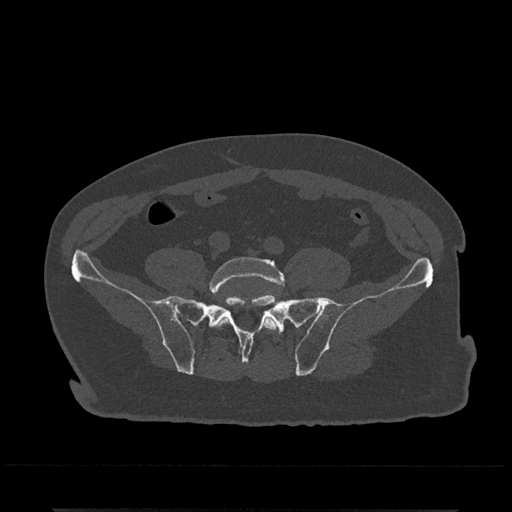
CT including the spine, one axial slice. Position 51 of 797 along the scan axis. Reconstruction kernel Br40s/3. Bone window (W 1800 / L 400 HU). 0.5 mm slice thickness. 512 × 512 image matrix, field of view 393 × 393 mm. Male patient, age 67 years. From the clinical record (not read from this slice): primary cancer: prostate.
Structures marked on this image (semi-automatic segmentation, software-assisted and operator-edited):
- L5 vertebra: bounding box [x1, y1, x2, y2] px = [209, 257, 285, 331]